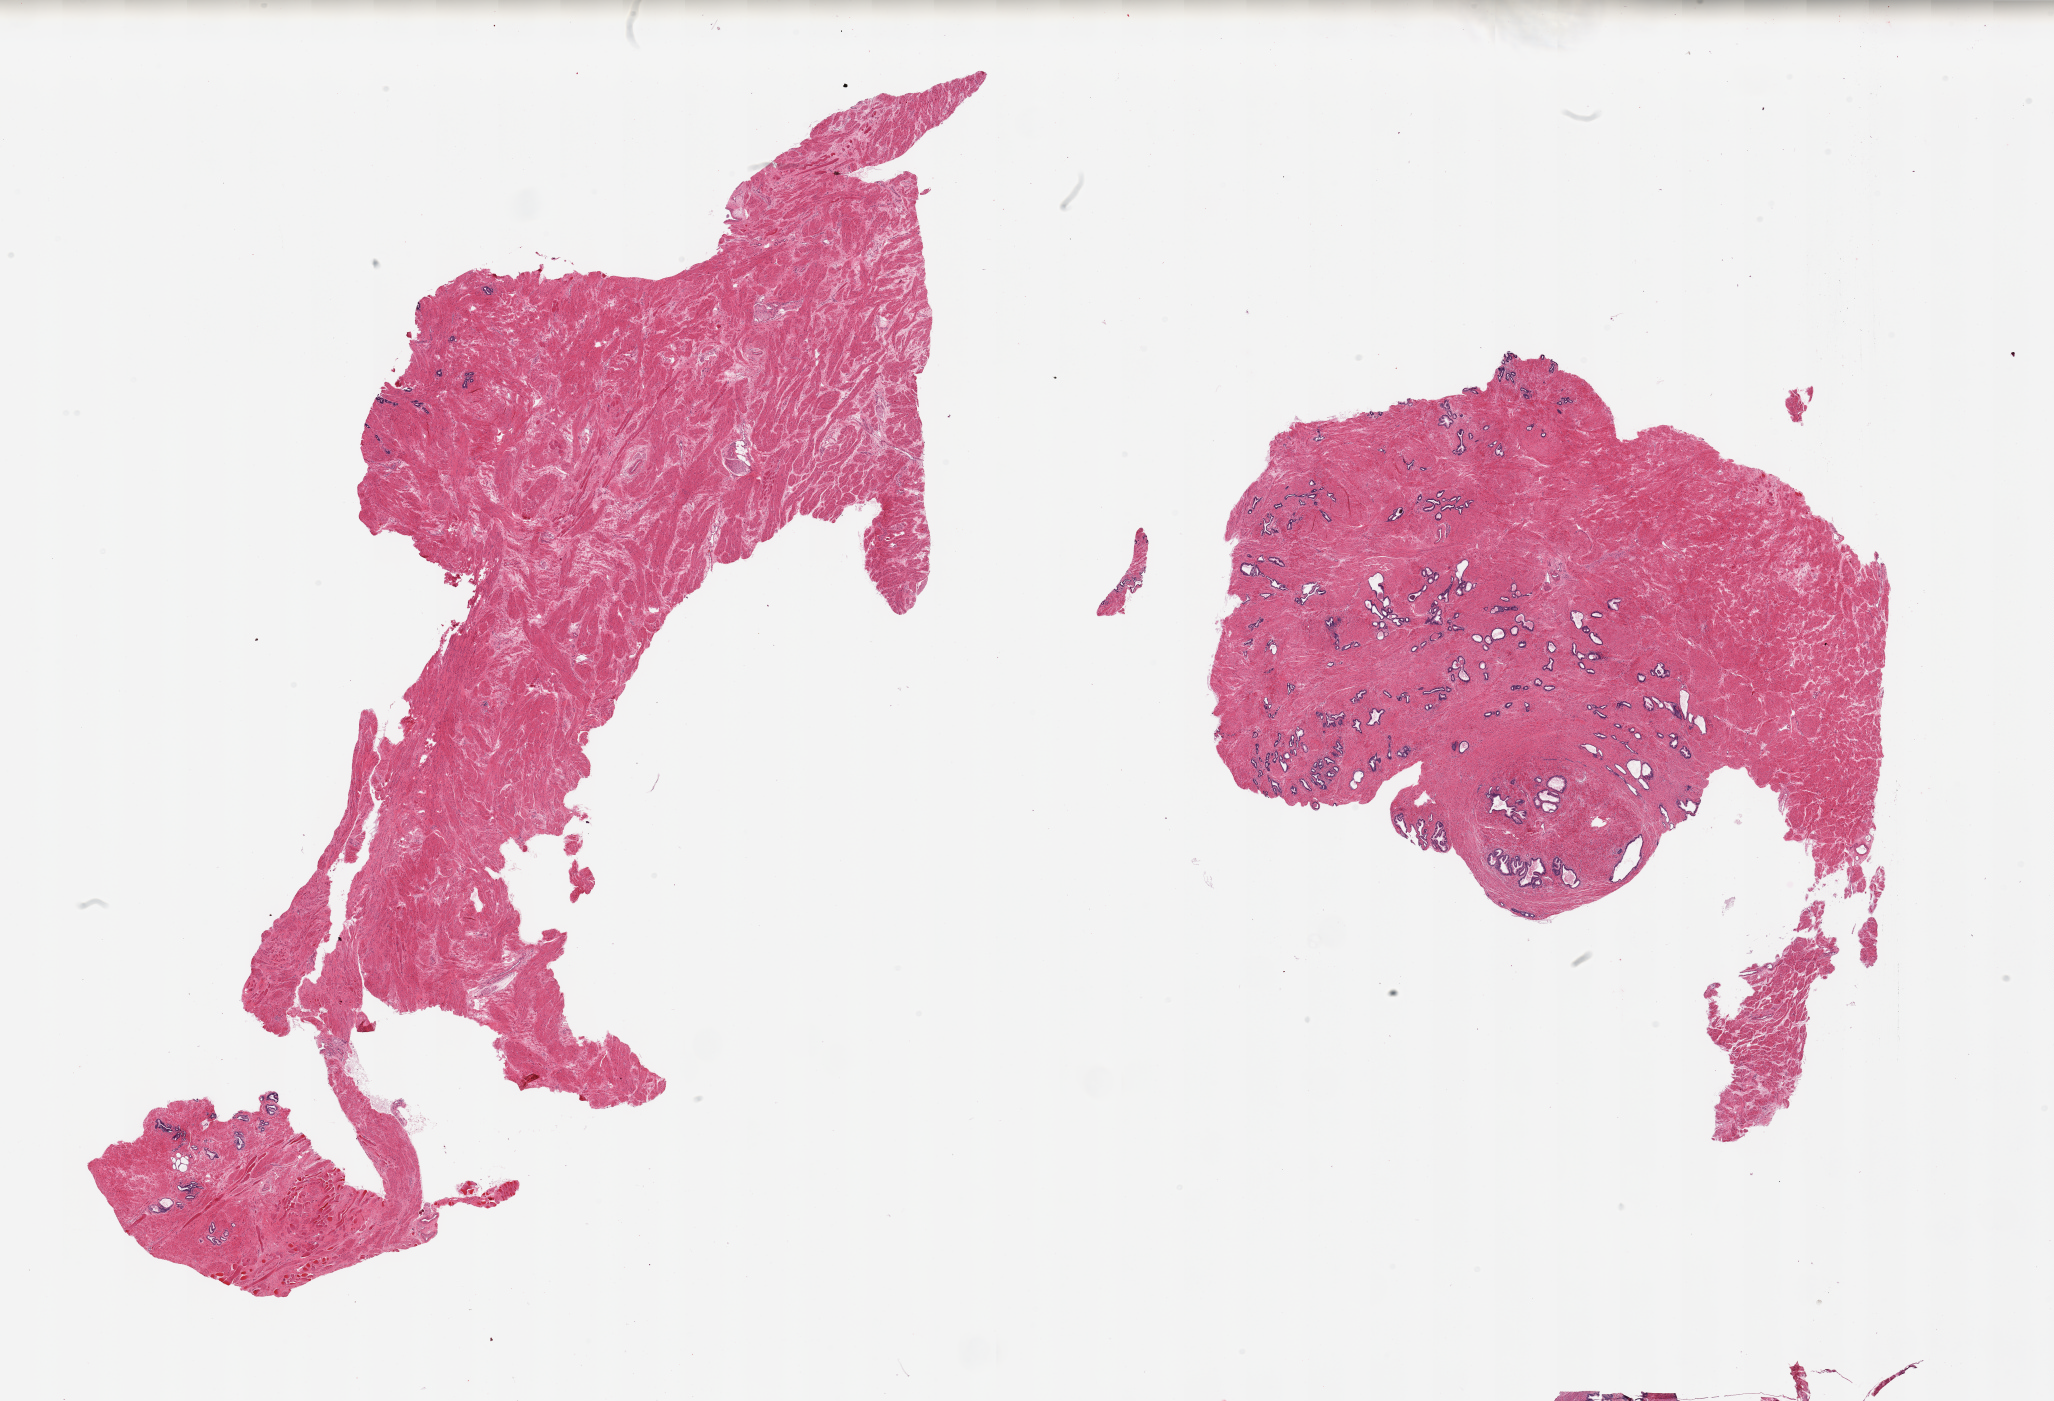
Whole-slide image, hematoxylin and eosin (H&E) stain — whole scanned area (about 32.5 x 22.2 mm) shown as a low-resolution overview. PAXgene-fixed, paraffin-embedded tissue. Target tissue: prostate. Donor tissue sample. Donor sex: male.
- pathologist's review note for this sample: 2 pieces, no abnormality; one section largely glandular stroma